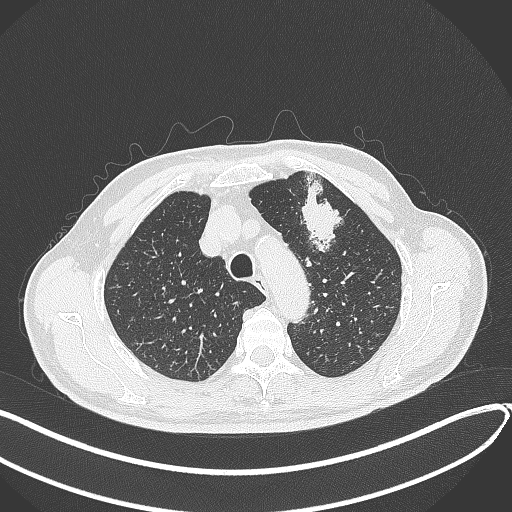
Chest CT, one axial slice. Slice 332 of 459 in the series (ordered by position). Reconstruction kernel B70f. Lung window (W 1500 / L -600 HU). 1 mm slice thickness. 512 × 512 image matrix. Male patient, age 74 years. From the clinical record (not read from this slice): clinical TNM (as recorded): T2b N0 M1c.
Outlined on this slice (bounding box drawn by a radiologist):
- lung tumour (recorded histology: adenocarcinoma): bounding box (x1, y1, x2, y2) in pixels: (291, 178, 341, 258)